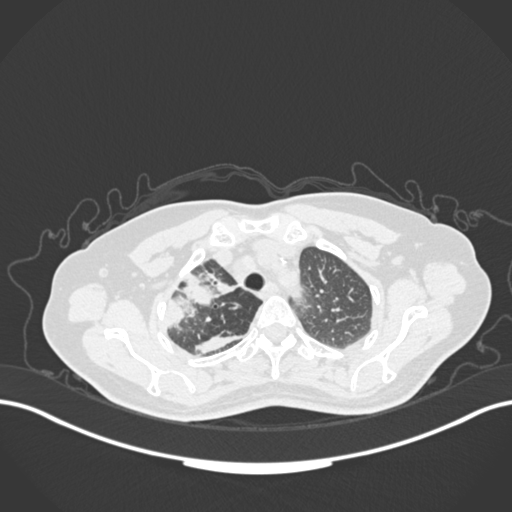
Chest CT, one axial slice; slice 132 of 177 in the series (ordered by position); reconstruction kernel B30f; lung window (W 1500 / L -600 HU); 1 mm slice thickness; 512 × 512 image matrix. Patient: female, 60 years. Case-level facts recorded for this patient, not image findings: clinical TNM (as recorded): T3 N1 M1.
Outlined on this slice (bounding box drawn by a radiologist):
- lung tumour (recorded histology: adenocarcinoma): bounding box (x1, y1, x2, y2) in pixels: (152, 252, 228, 331)